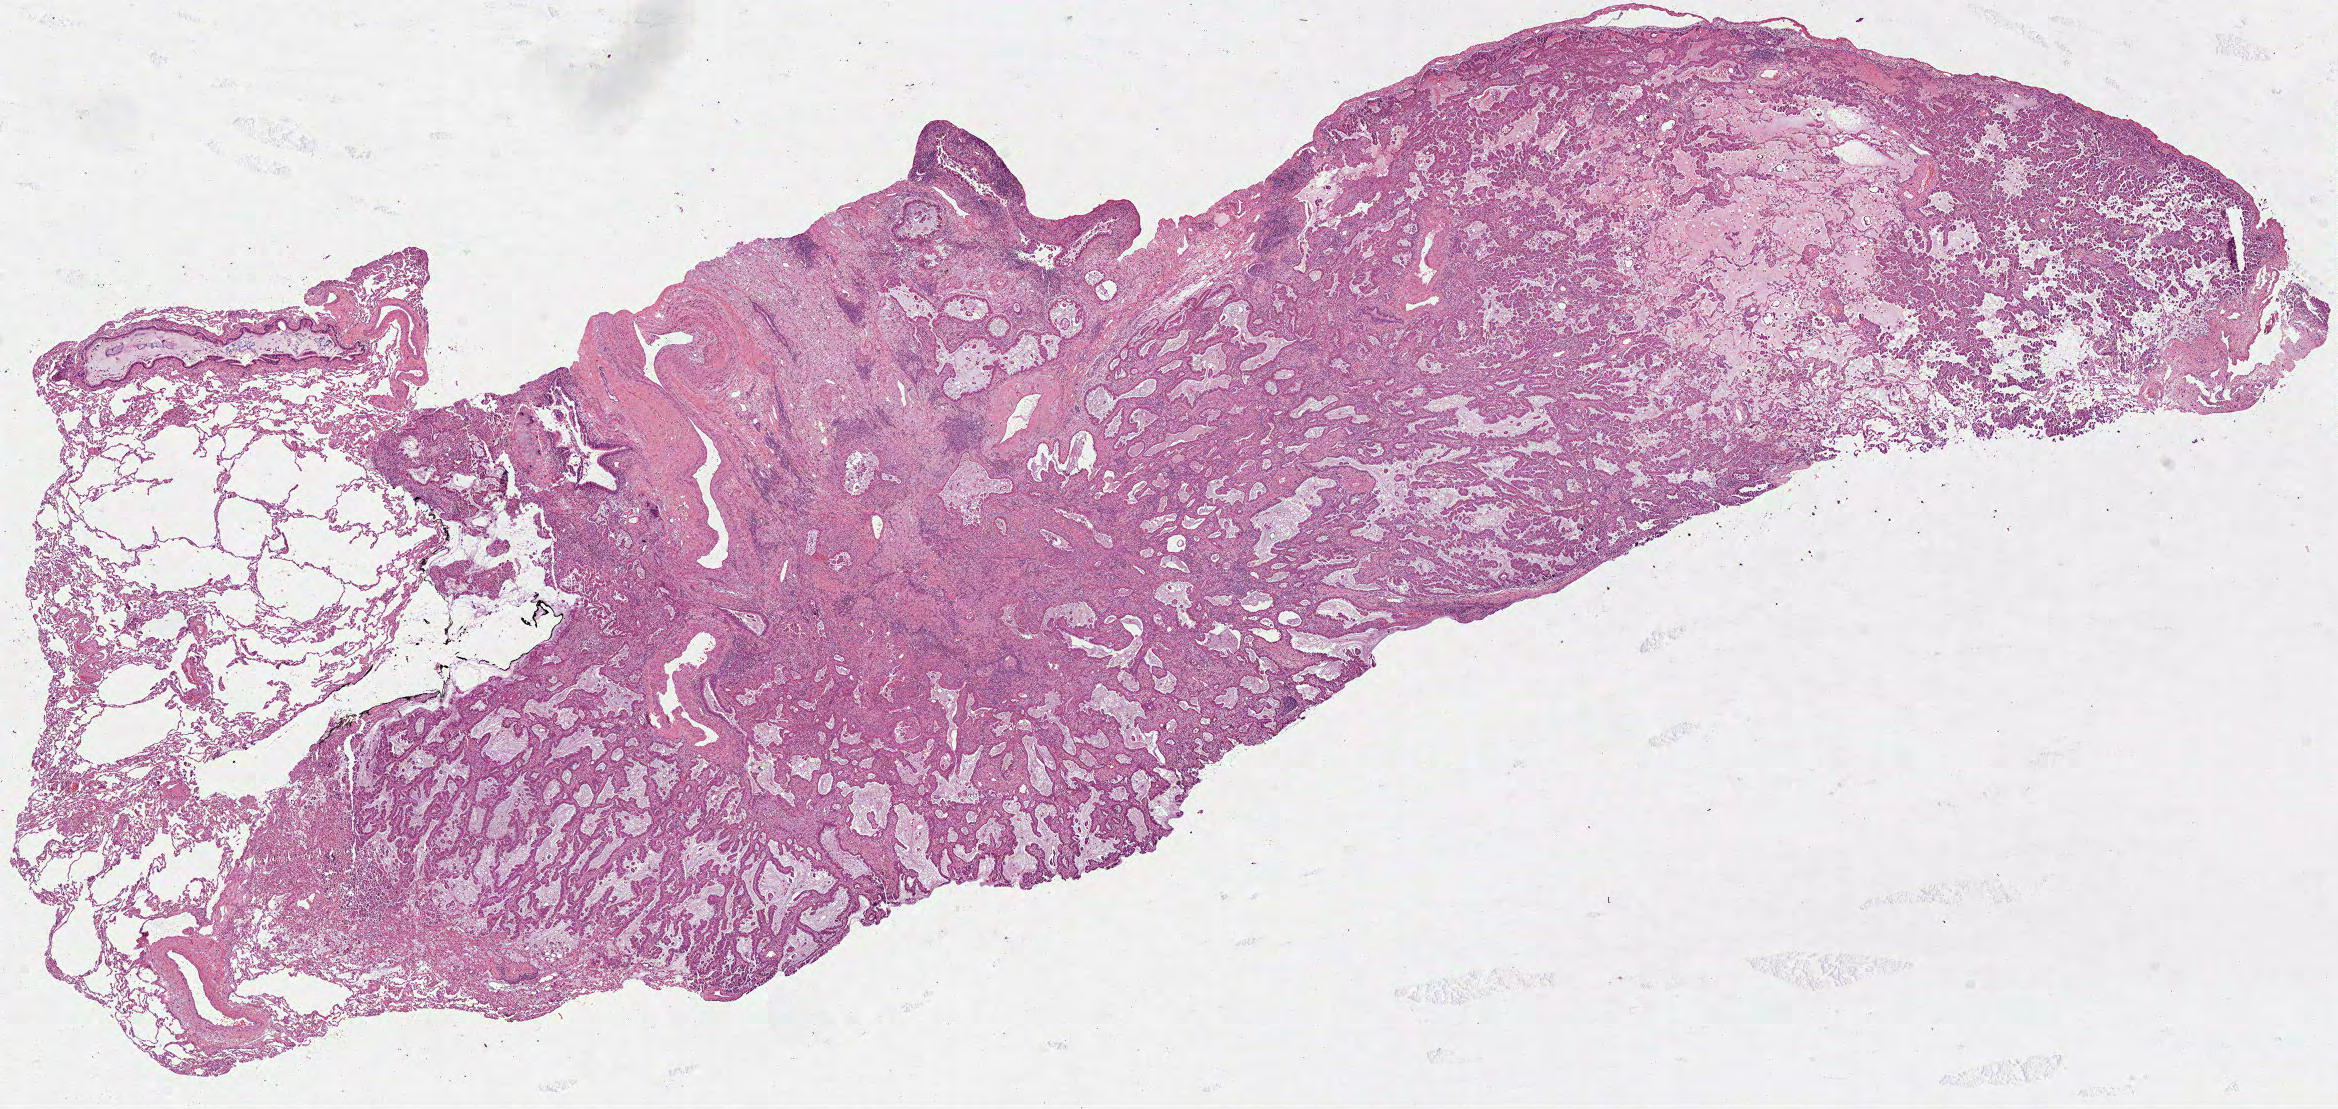
H&E whole-slide image, low-resolution overview of the scanned area, about 18.9 x 8.9 mm (slide scanned at 40x), formalin-fixed paraffin-embedded (FFPE) diagnostic section, lung, primary tumour sample. Female, age 74 years at initial diagnosis.
* AJCC pathologic stage: IB
* pathologic diagnosis: Bronchiolo-alveolar carcinoma, non-mucinous
* laterality: right